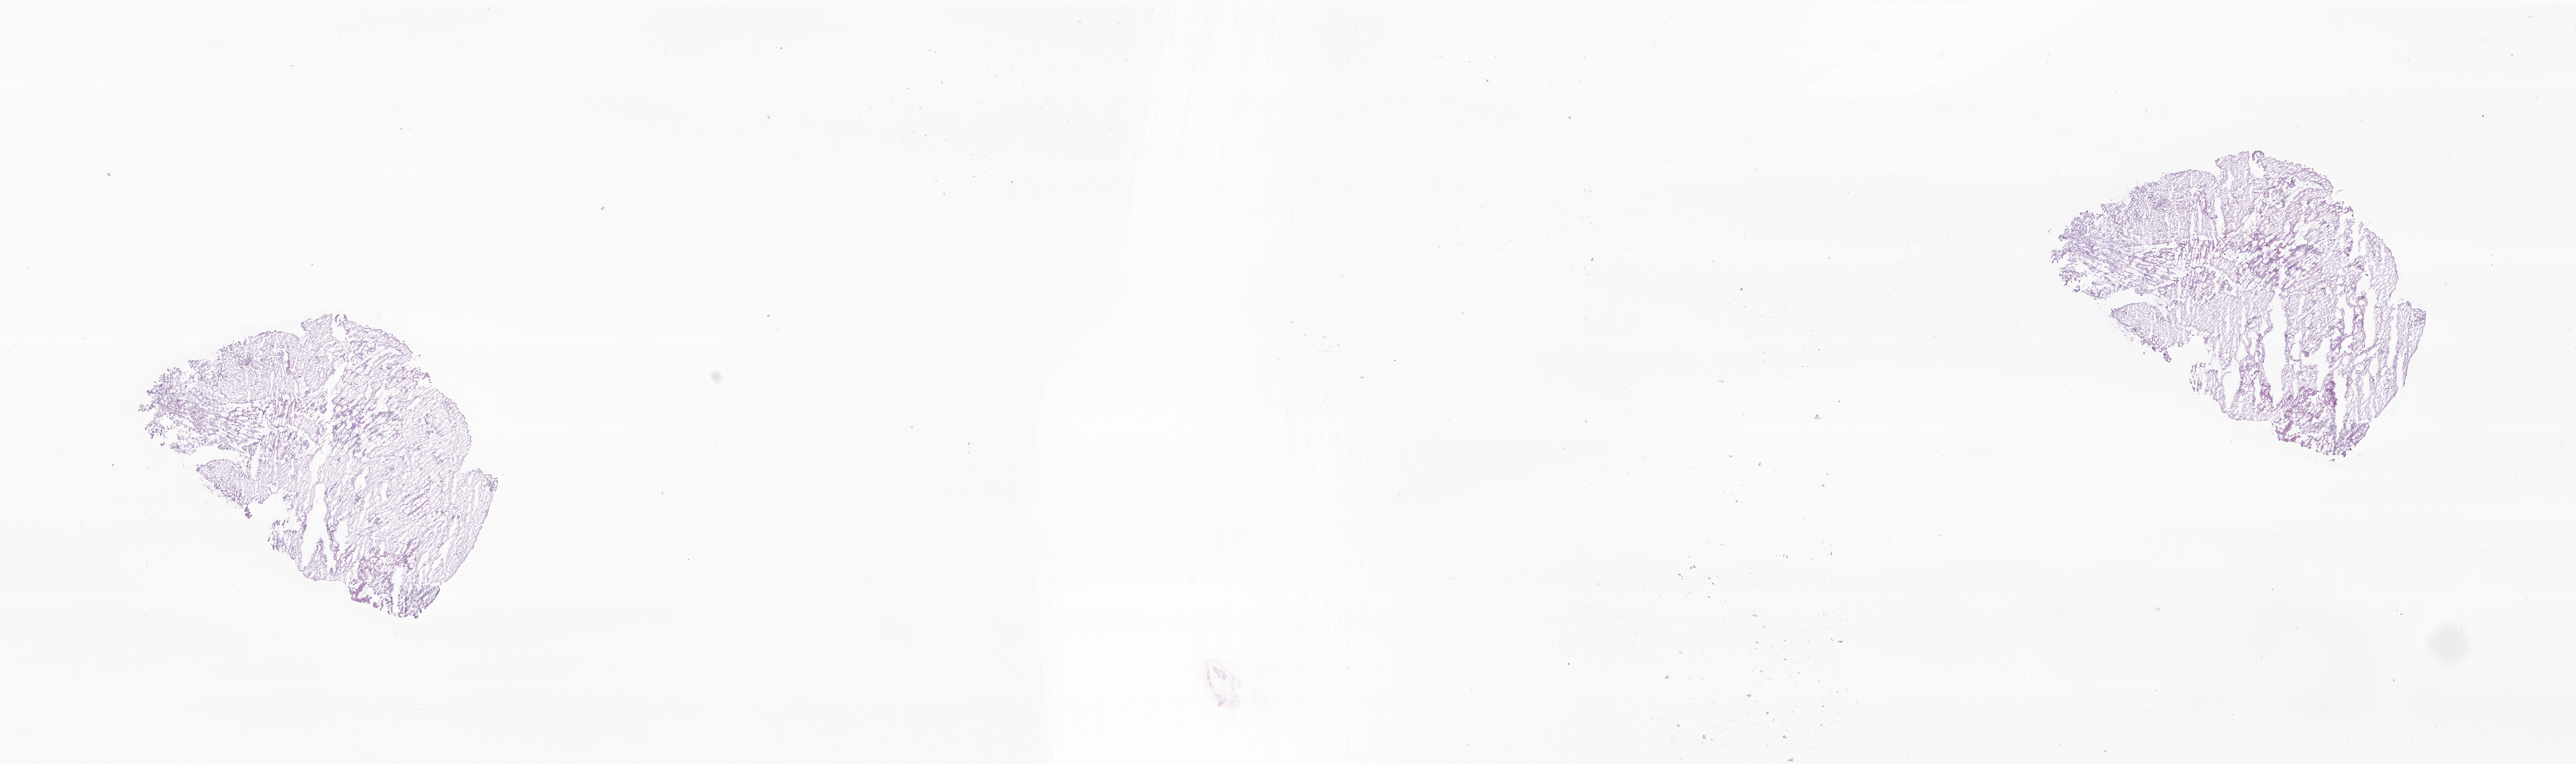
Whole-slide image, haematoxylin and eosin stain of tumor tissue from the brain — low-resolution overview of the scanned area, about 31.9 x 9.5 mm, cryosection (OCT / tissue freezing medium). Patient male; age 46 months (3 years 10 months).
Diagnosis (ICD-O-3 morphology term): Glioma, malignant.